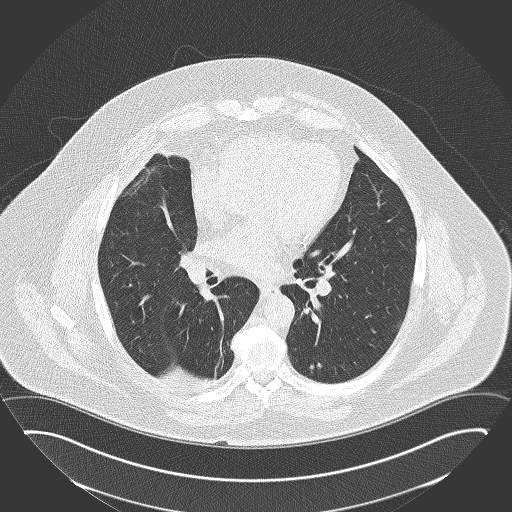
Chest CT (low-dose screening protocol), one axial image; second annual screen; lung window (W 1500 / L -600 HU); lung (sharp) reconstruction kernel (B50f); slice 97 of 180 in the series. Male participant, aged 63 years at enrolment. Former smoker at enrolment.
Lesion marked by an expert reader, bounding box <289,349,334,389> (left, top, right, bottom; pixels). Reader record for this screening exam (exam-level; its link to the box is not recorded): non-calcified nodule or mass ≥4 mm, left lower lobe, 12 × 12 mm, poorly defined margins, ground glass attenuation, pre-existing on the prior screen: no. Official screen result: positive, other. Later outcome: lung cancer diagnosed 550 days after this screen — squamous cell carcinoma, NOS, left lower lobe, moderately differentiated (G2), stage IA (AJCC 6th edition), 15 mm at pathology.